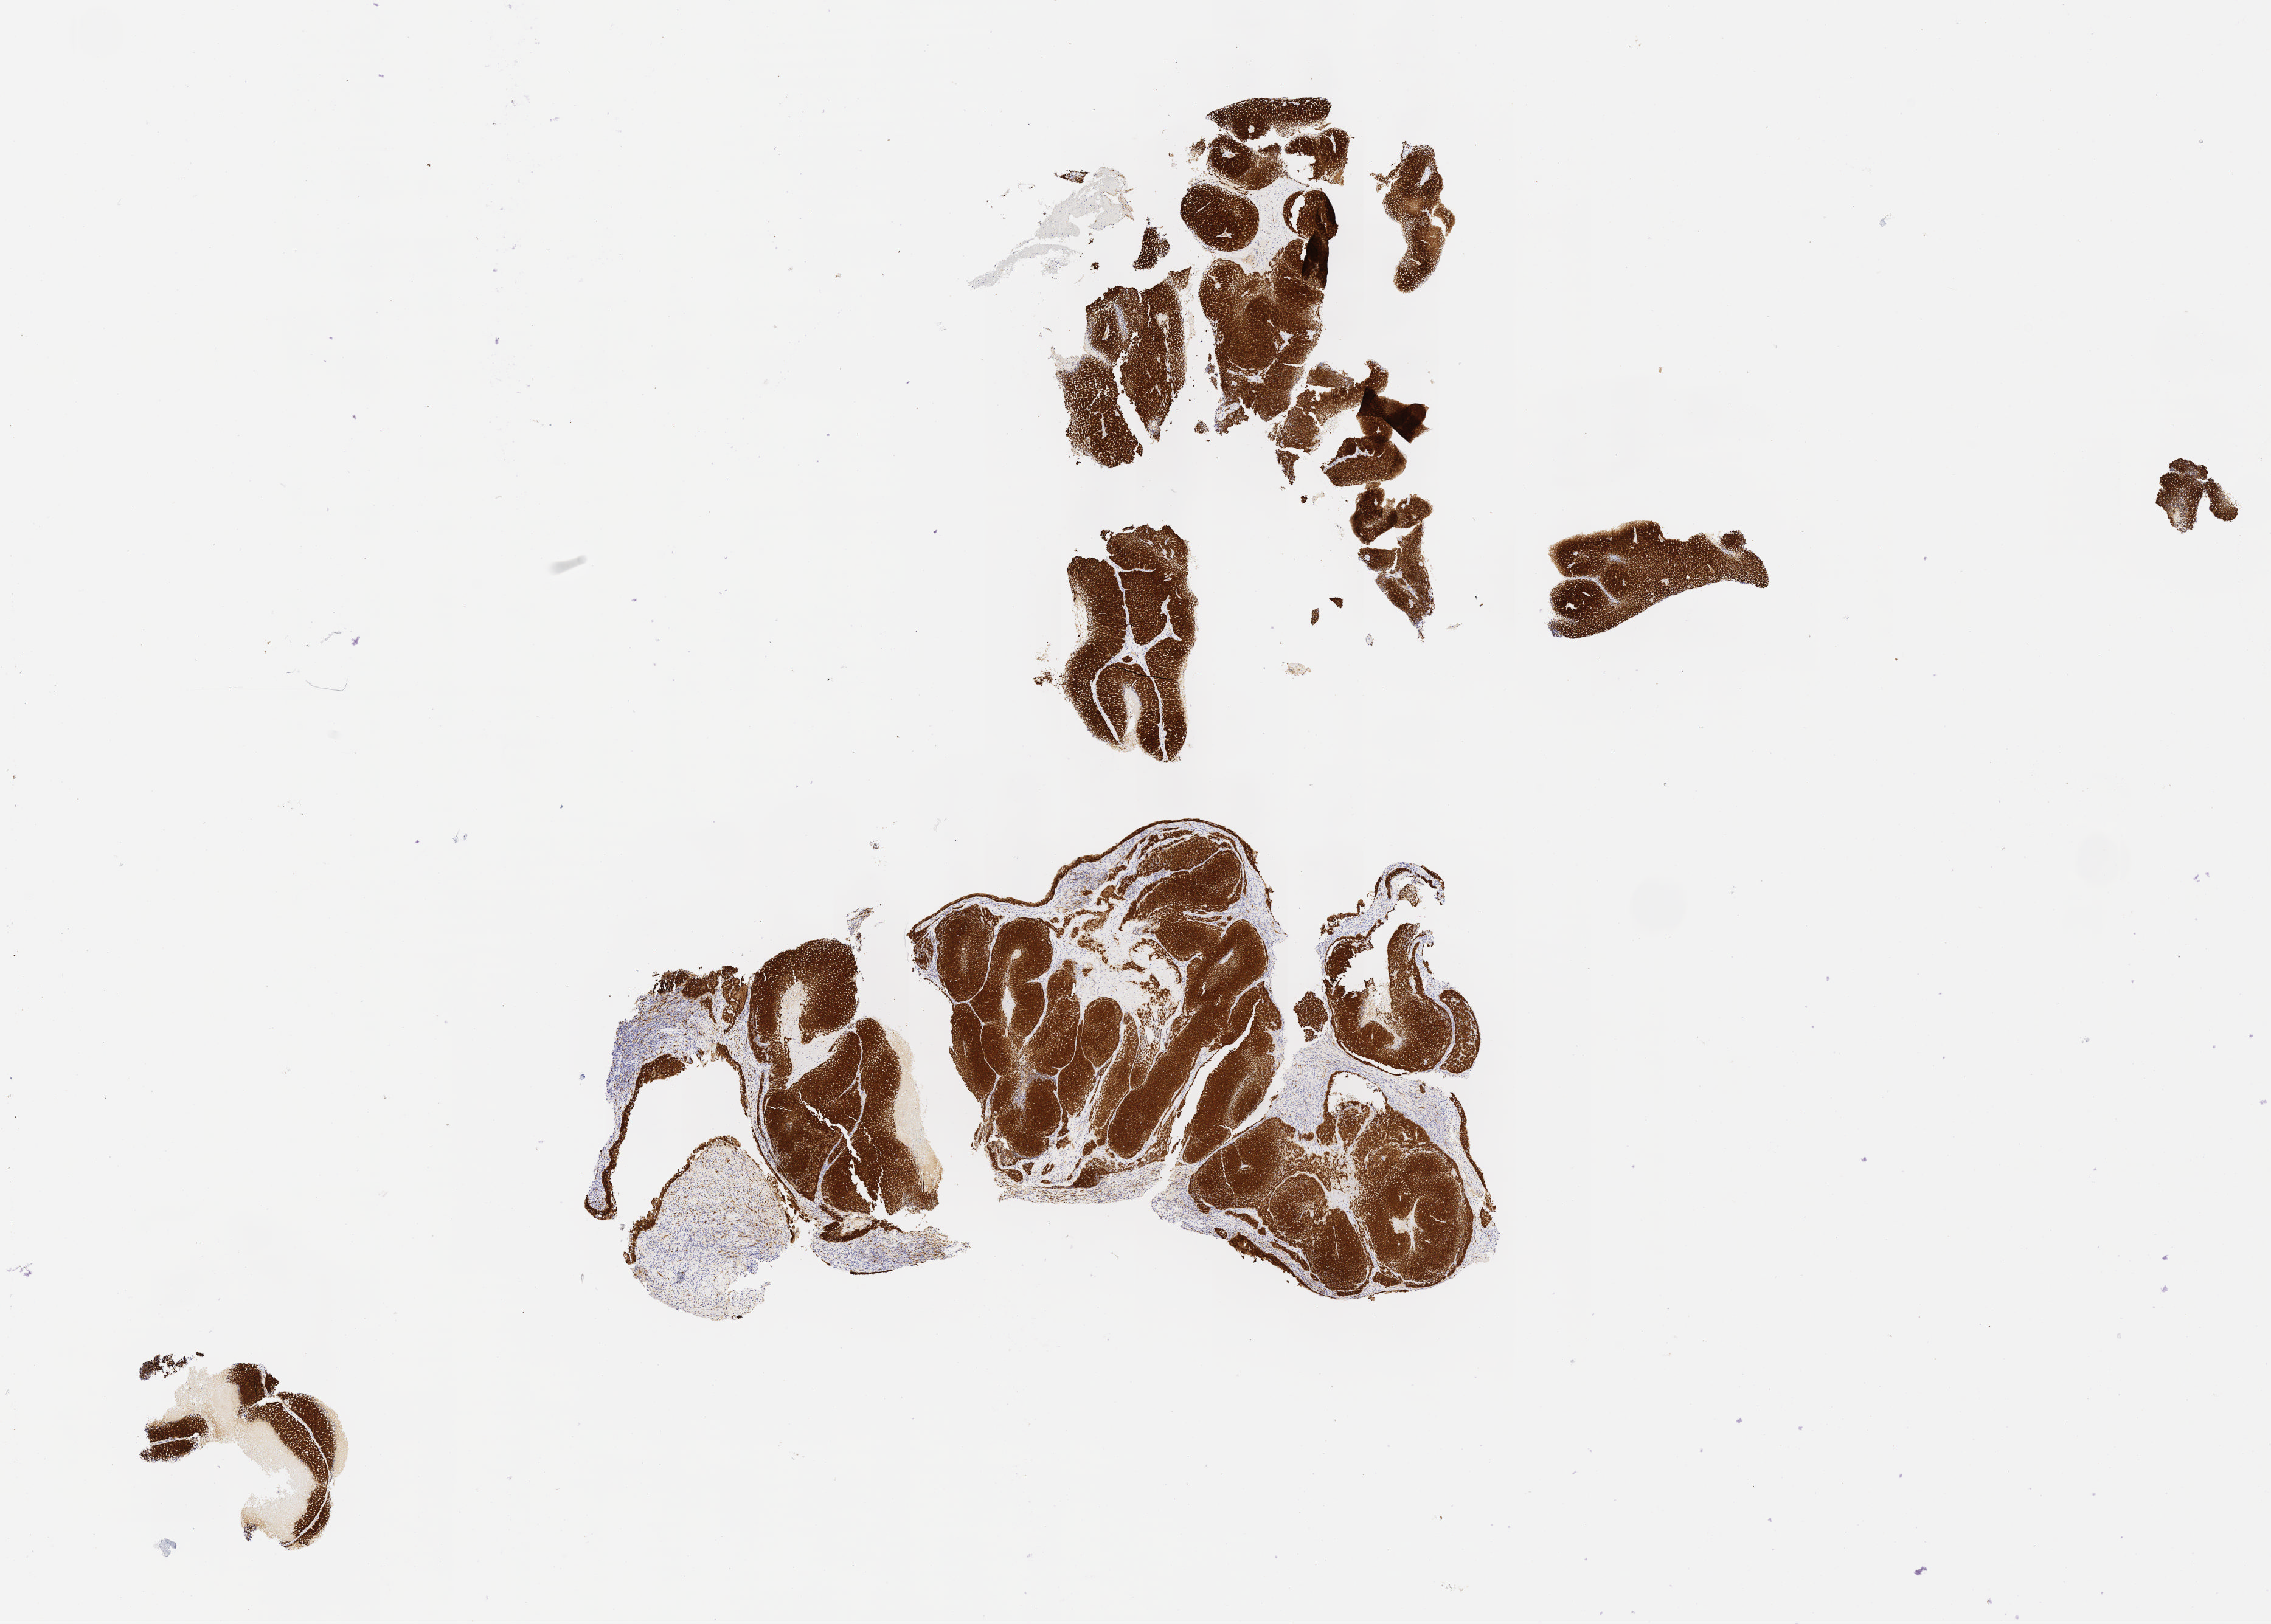
Immunohistochemistry (IHC) whole-slide image stained for p16 (p16INK4a) — low-resolution overview of the scanned area, about 15.1 x 10.8 mm; tumor tissue; site: cervix. Patient female; 71 years old.
• diagnosis: Squamous cell carcinoma, large cell, nonkeratinizing, NOS